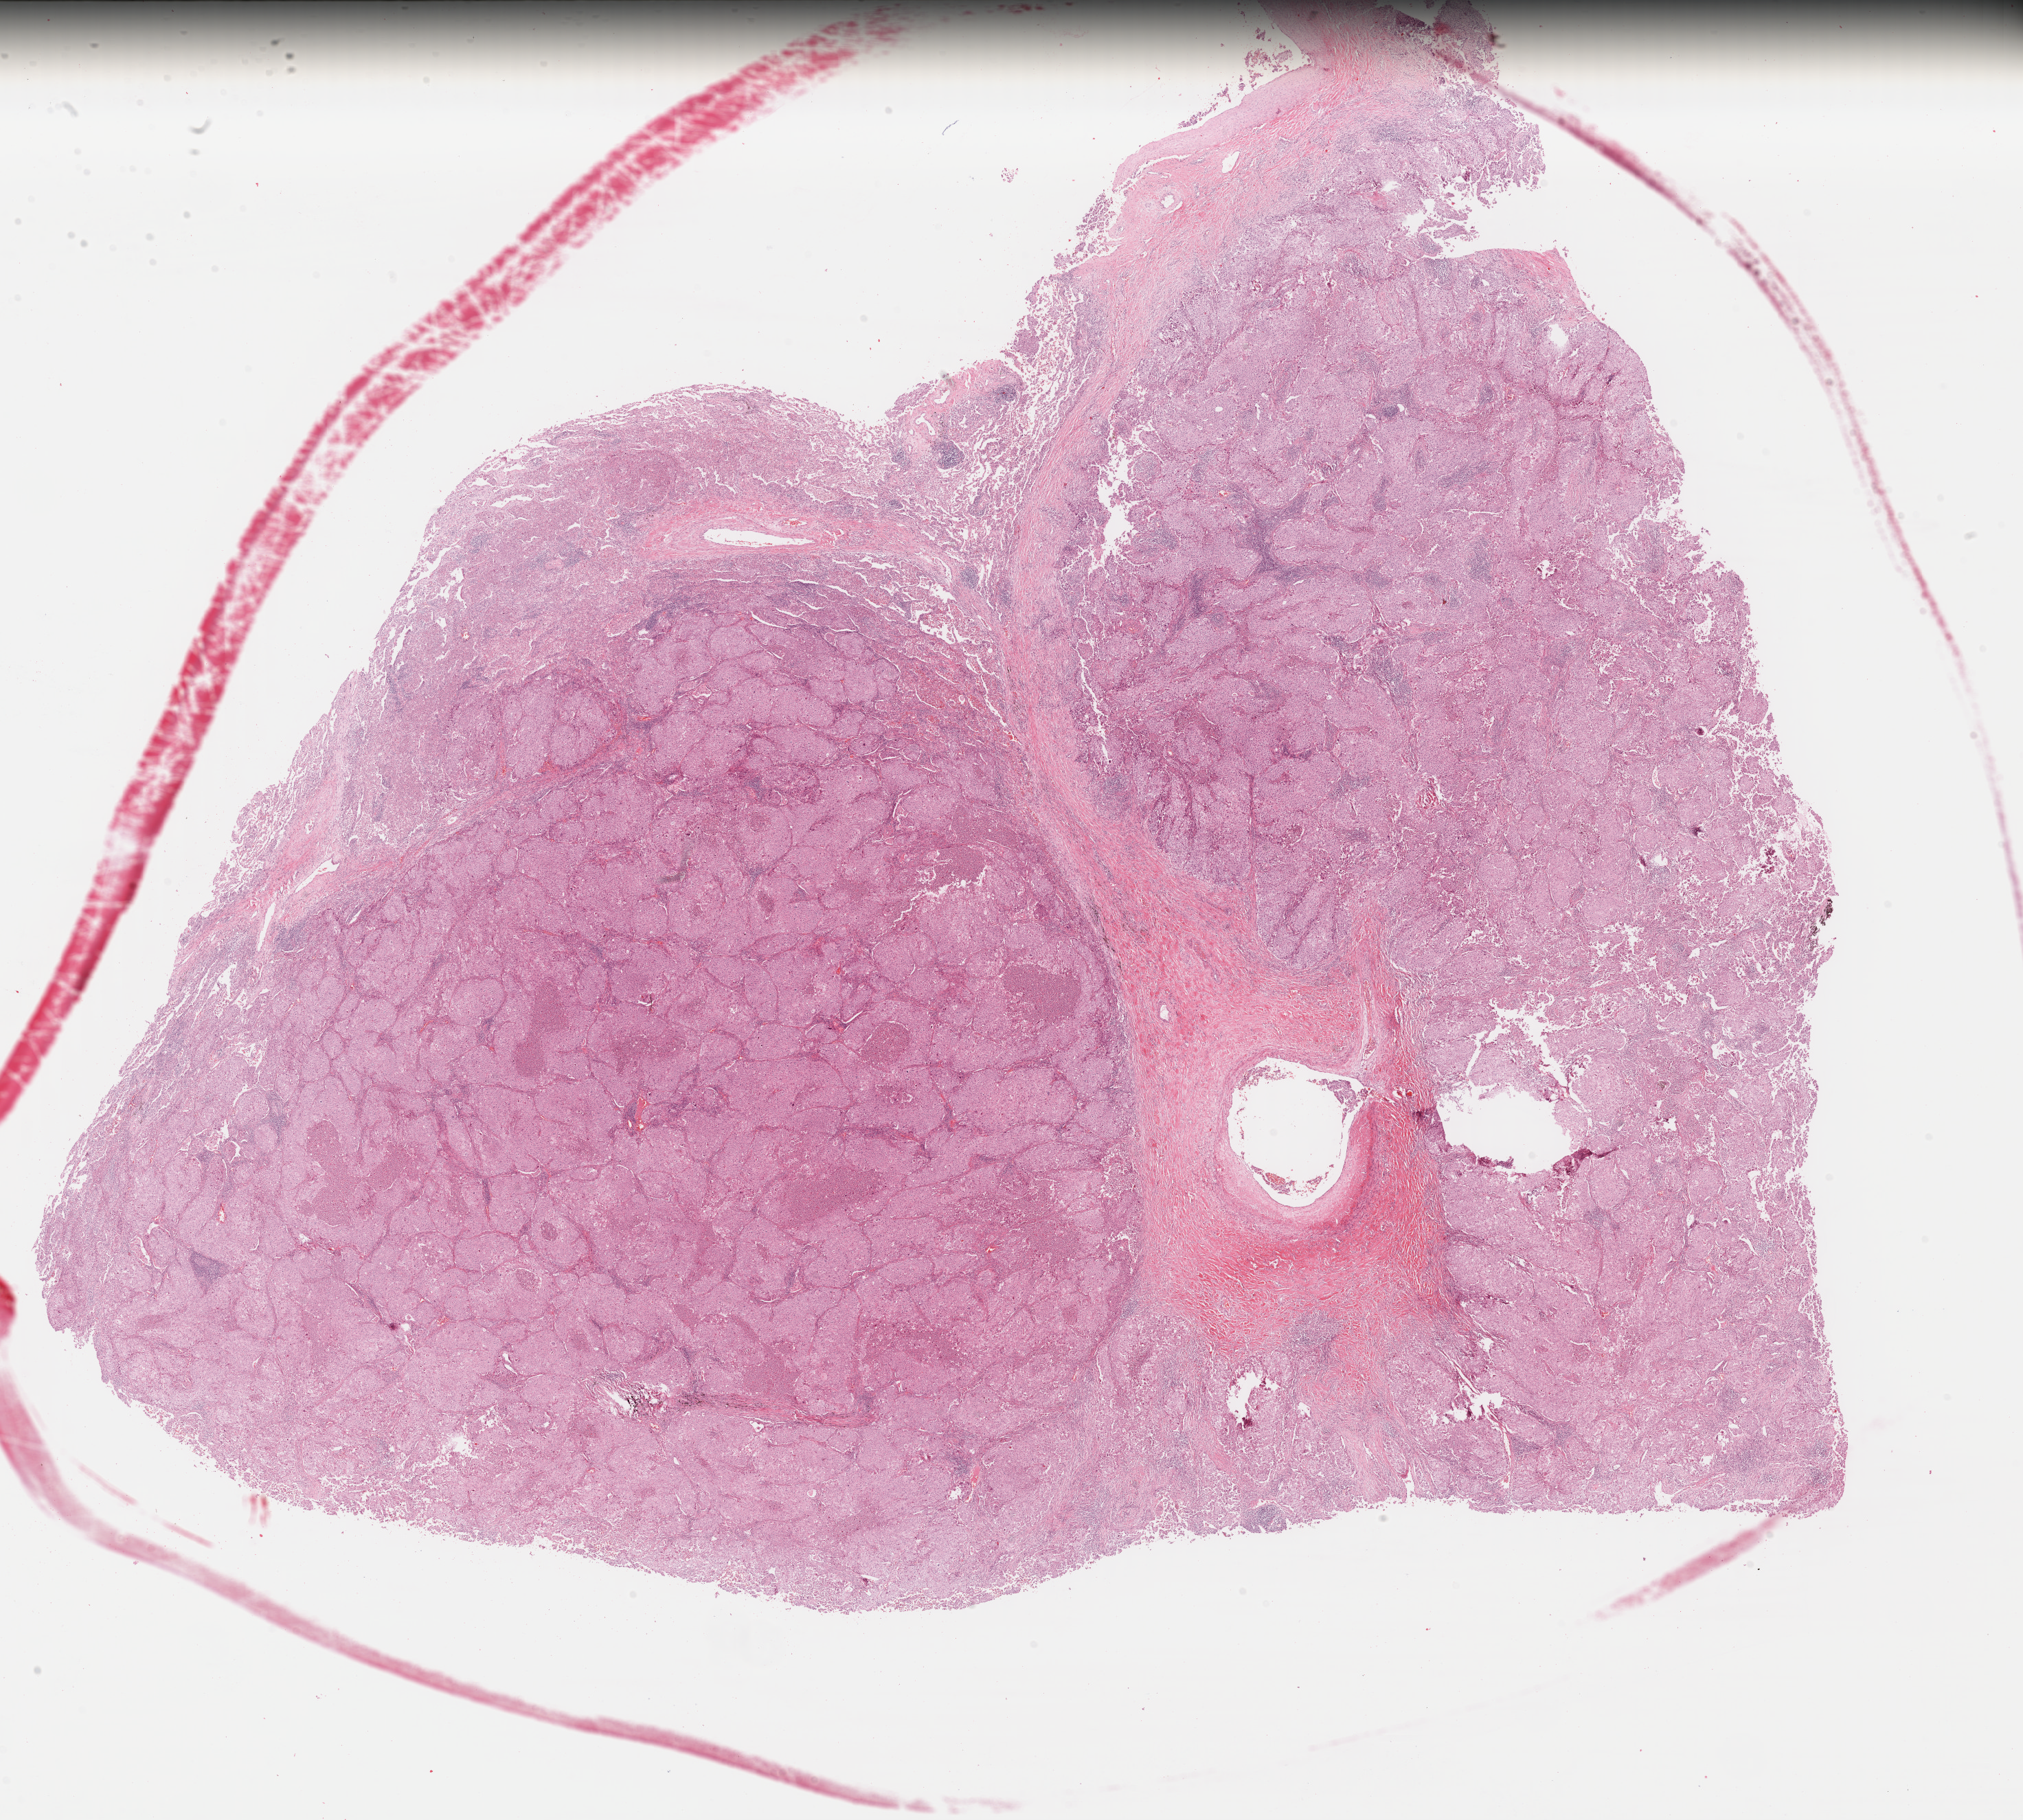
Digitized H&E tissue section (whole slide) — a low-resolution overview of the entire scanned area, about 23.1 x 20.8 mm; formalin-fixed paraffin-embedded (FFPE) diagnostic section; primary tumour sample from the lung. Male, age 57 years at initial diagnosis.
Pathologic diagnosis: Squamous cell carcinoma, NOS (upper lobe, lung).